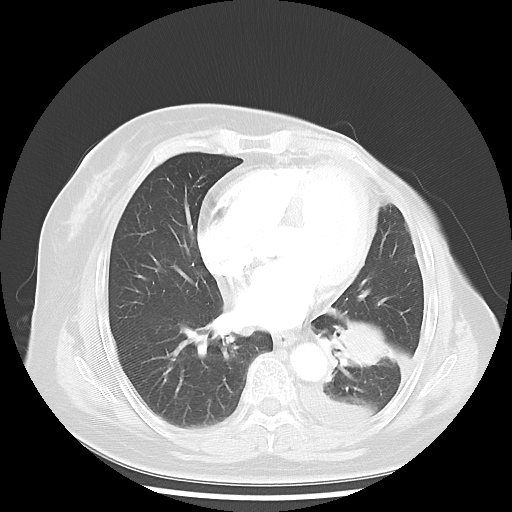
Chest CT, one axial slice; position 19 of 48 along the scan axis; reconstruction kernel LUNG; 120 kVp; lung window (W 1500 / L -600 HU); 5 mm slice thickness; 512 × 512 image matrix. Female patient, age 63 years. From the clinical record (not read from this slice): clinical TNM (as recorded): T2 N0 M1.
Structures marked on this image (rectangle marked by the reading radiologist):
- lung tumour (recorded histology: adenocarcinoma): bounding box (x1, y1, x2, y2) in pixels: (330, 318, 395, 384)